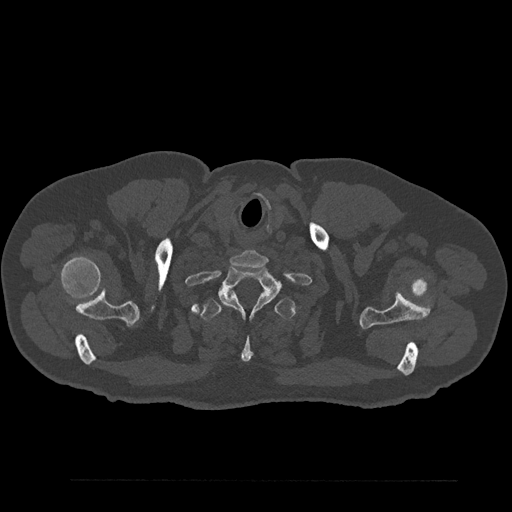
CT including the spine, one axial slice. Slice 745 of 797 in the series (ordered by position). Reconstruction kernel Br40s/3. 120 kVp. Bone window (W 1800 / L 400 HU). 0.5 mm slice thickness. 512 × 512 image matrix, field of view 430 × 430 mm. Patient: male, 61 years. Case-level facts recorded for this patient, not image findings: primary cancer: prostate.
Outlined on this slice (semi-automatic segmentation, software-assisted and operator-edited):
- T1 vertebra: bounding box [x1, y1, x2, y2] px = [218, 268, 279, 316]
- T2 vertebra: [200, 292, 295, 362]